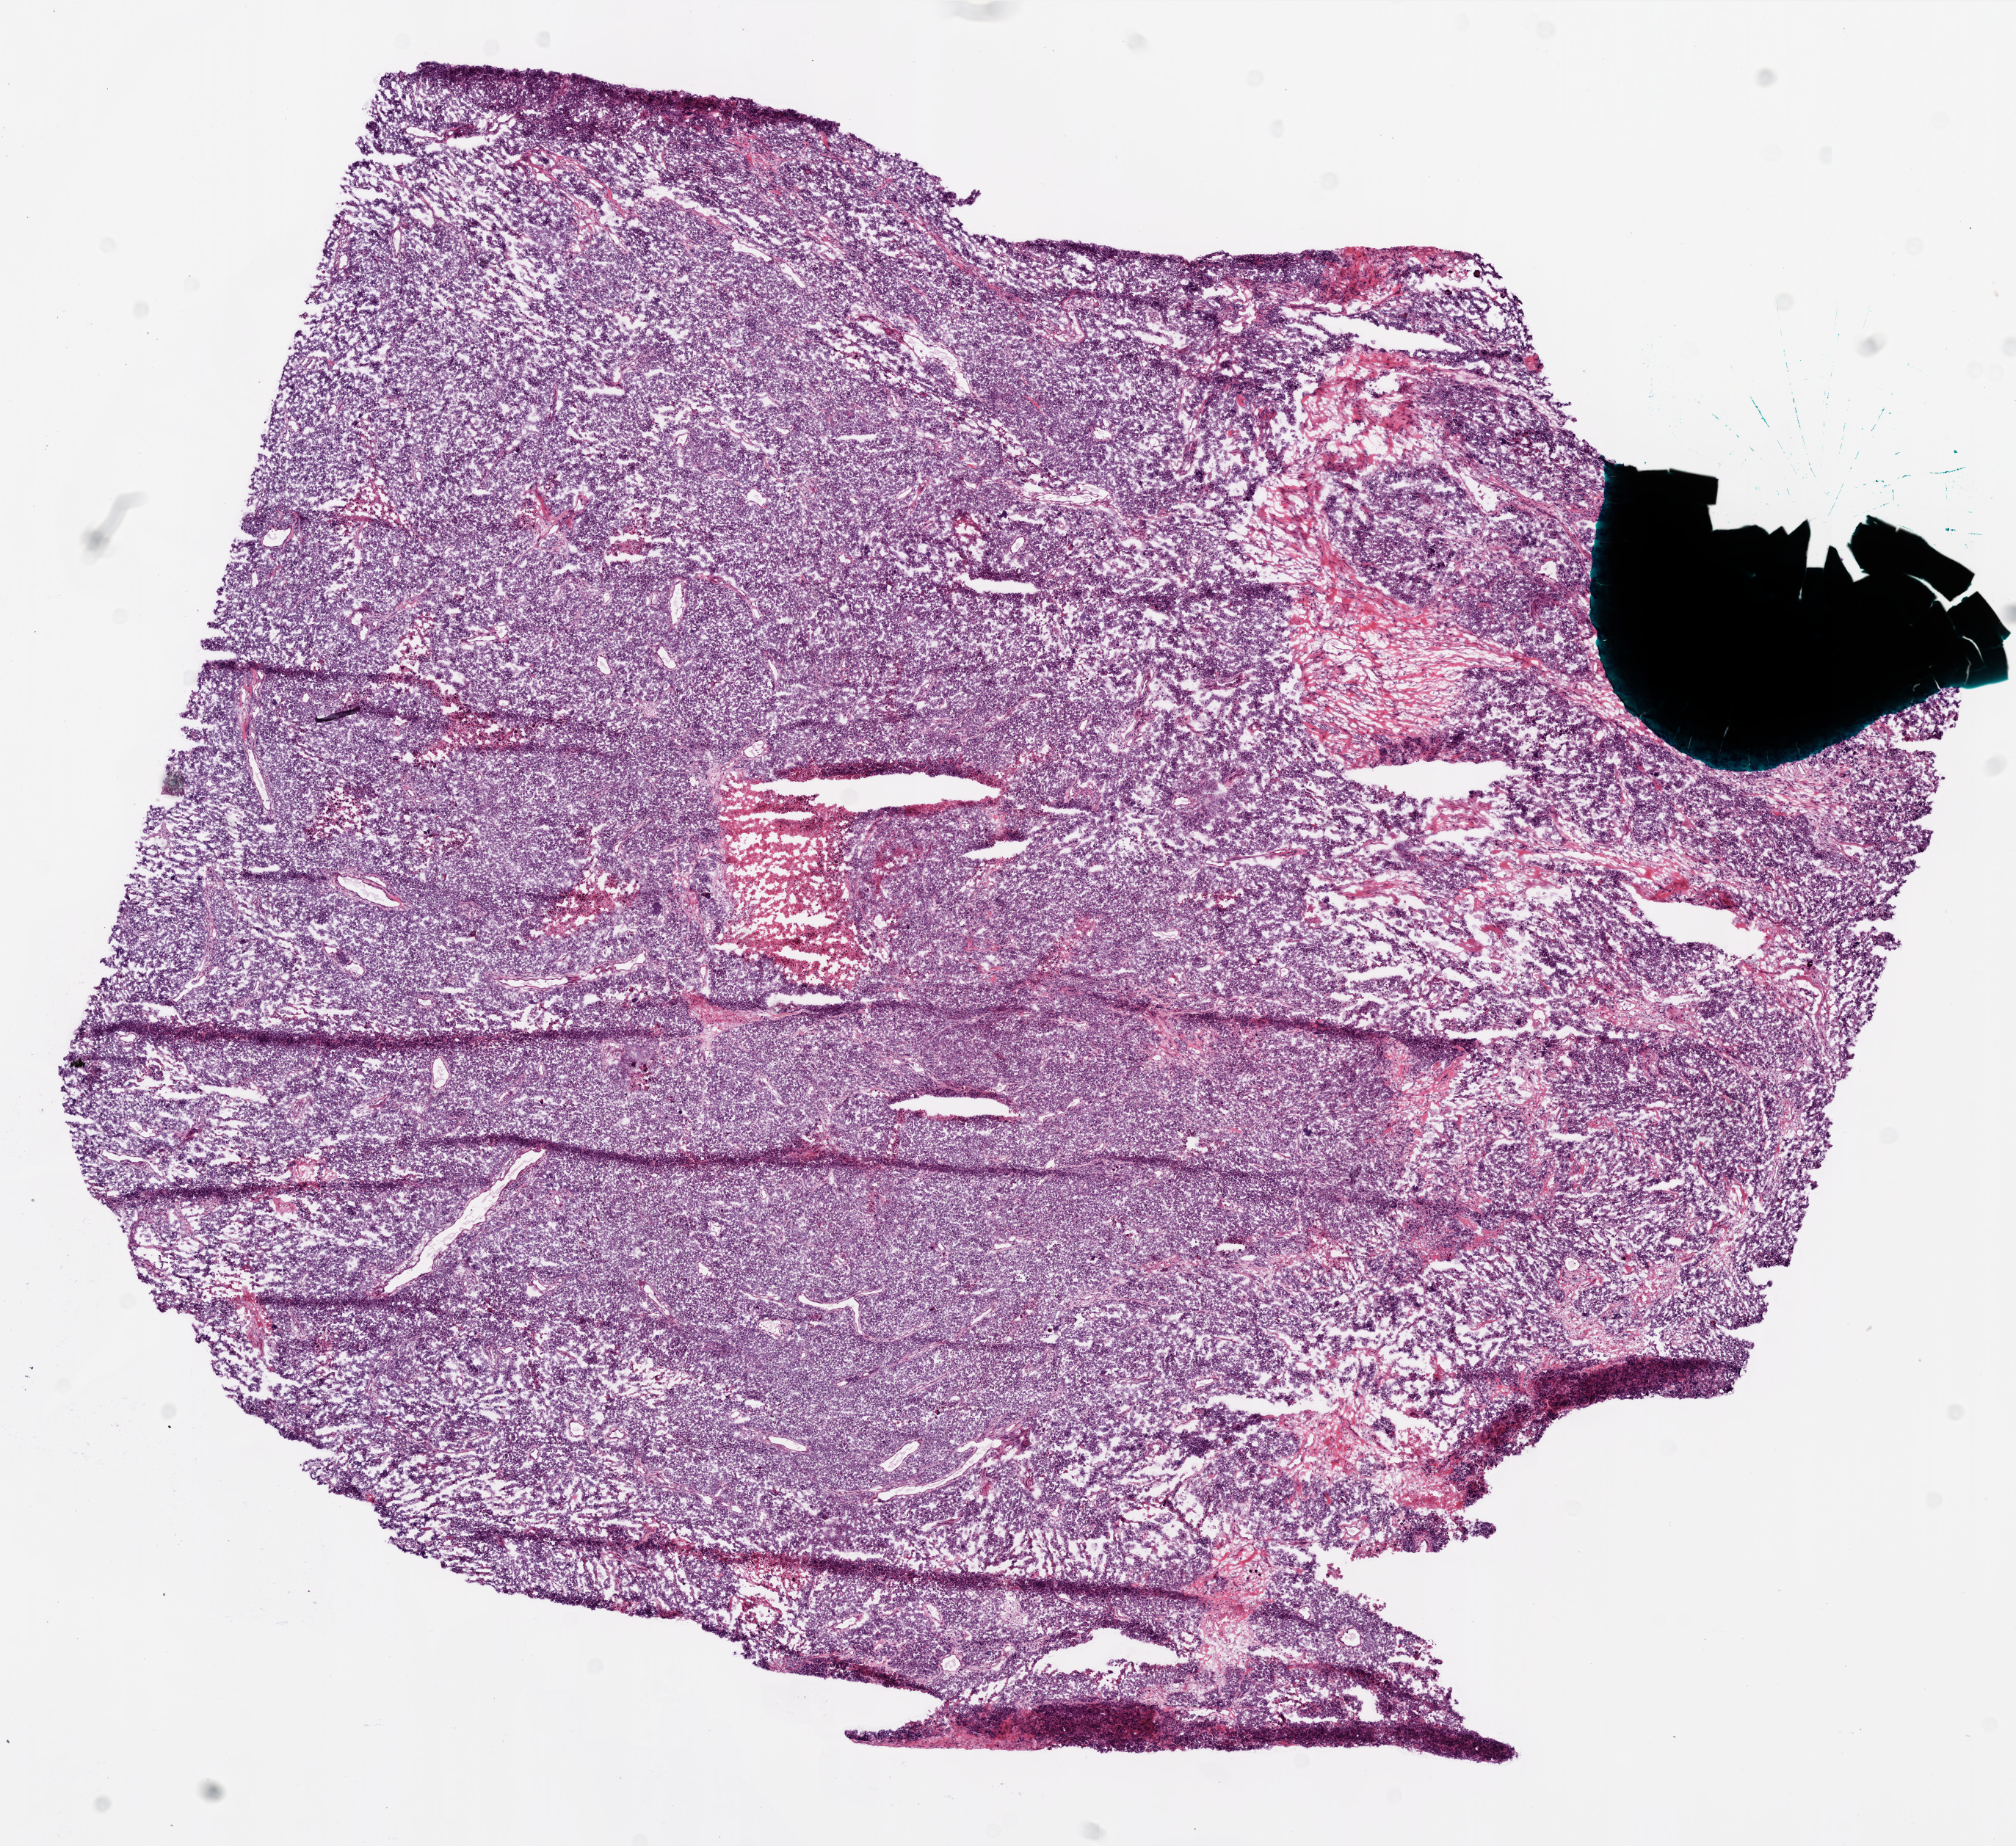
Digitized Hematoxylin and eosin (H&E) stained tissue section (whole slide), a low-resolution overview of the entire scanned area, about 11.0 x 10.1 mm (acquisition: 20x scan). Frozen section from the bottom of the tissue portion. Primary tumour sample from the ovary. Patient: female, age at initial diagnosis 51 years. Histologic grade: G3 (poorly differentiated). Slide review estimates, as recorded: tumour cells 0%, tumour nuclei 95%, normal cells 0%, stromal cells 0%, necrosis 5%.
Diagnosis: Serous cystadenocarcinoma, NOS. FIGO stage: IIIC.